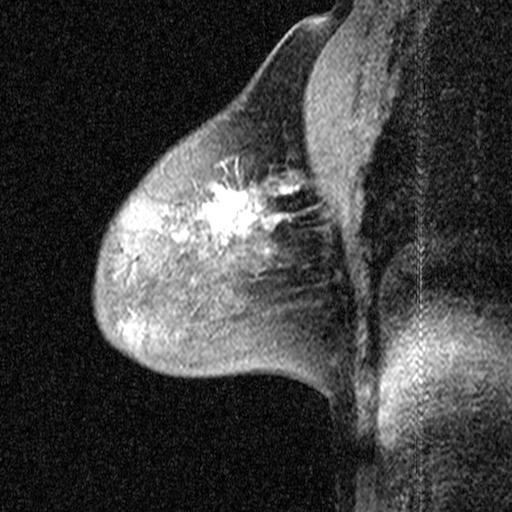
Breast MRI (dynamic contrast-enhanced), one sagittal slice. Slice 29 of 44 in the series (ordered by position). Dynamic contrast-enhanced study with each time point stored as its own series, time point 2 of 3 at this slice position (early post-contrast, ordered by acquisition time). 1.5 T. TE 4.5 ms, TR 11 ms. 3 mm slice thickness. 512 × 512 image matrix. Female patient, age 53 years. From the clinical record (not read from this slice): setting: breast cancer imaged before/during neoadjuvant chemotherapy; receptor status: HR-positive, HER2-negative.
Annotated regions visible in this slice (semi-automatically segmented with operator editing):
- analysis volume of interest (the breast-tissue region the enhancement analysis was run in; not a lesion): box from (x=198, y=152) to (x=299, y=267) px
- tumour enhancement mask (voxels above the 90 % enhancement threshold inside the analysis volume of interest): (x=200, y=186)–(x=298, y=230)